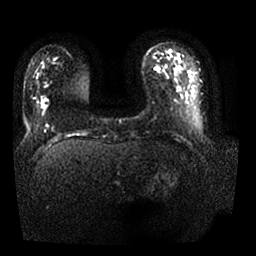
Breast MRI, one axial slice. Slice 7 of 25 in the series (ordered by position). Diffusion-weighted series; image 2 of 4 stored at this slice position (different b-values; order by instance number). 1.5 T. 4 mm slice thickness. 256 × 256 image matrix. Female patient.
Structures marked on this image (expert manual segmentation):
- tumour on diffusion-weighted imaging: bounding box [x1, y1, x2, y2] px = [42, 99, 48, 108]